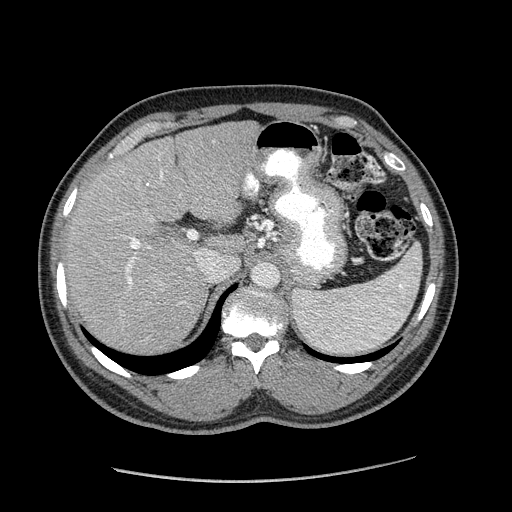
Contrast-enhanced abdominal CT (liver protocol), one axial slice. Position 125 of 182 along the scan axis. 120 kVp. Soft-tissue window (W 400 / L 40 HU). 512 × 512 image matrix, field of view 400 × 400 mm. Case-level facts recorded for this patient, not image findings: diagnosis: hepatocellular carcinoma (patient treated with transarterial chemoembolisation; whether this scan precedes or follows treatment is not stated here); TNM stage (as recorded): Stage-I; Child-Pugh class: A.
Outlined on this slice (semi-automatically segmented with operator editing):
- liver parenchyma outside the tumour (the mass and vessels are separate outlines, so this box may not span the whole liver): box from (x=66, y=120) to (x=260, y=352) px
- liver vessels: (x=126, y=158)–(x=201, y=304)